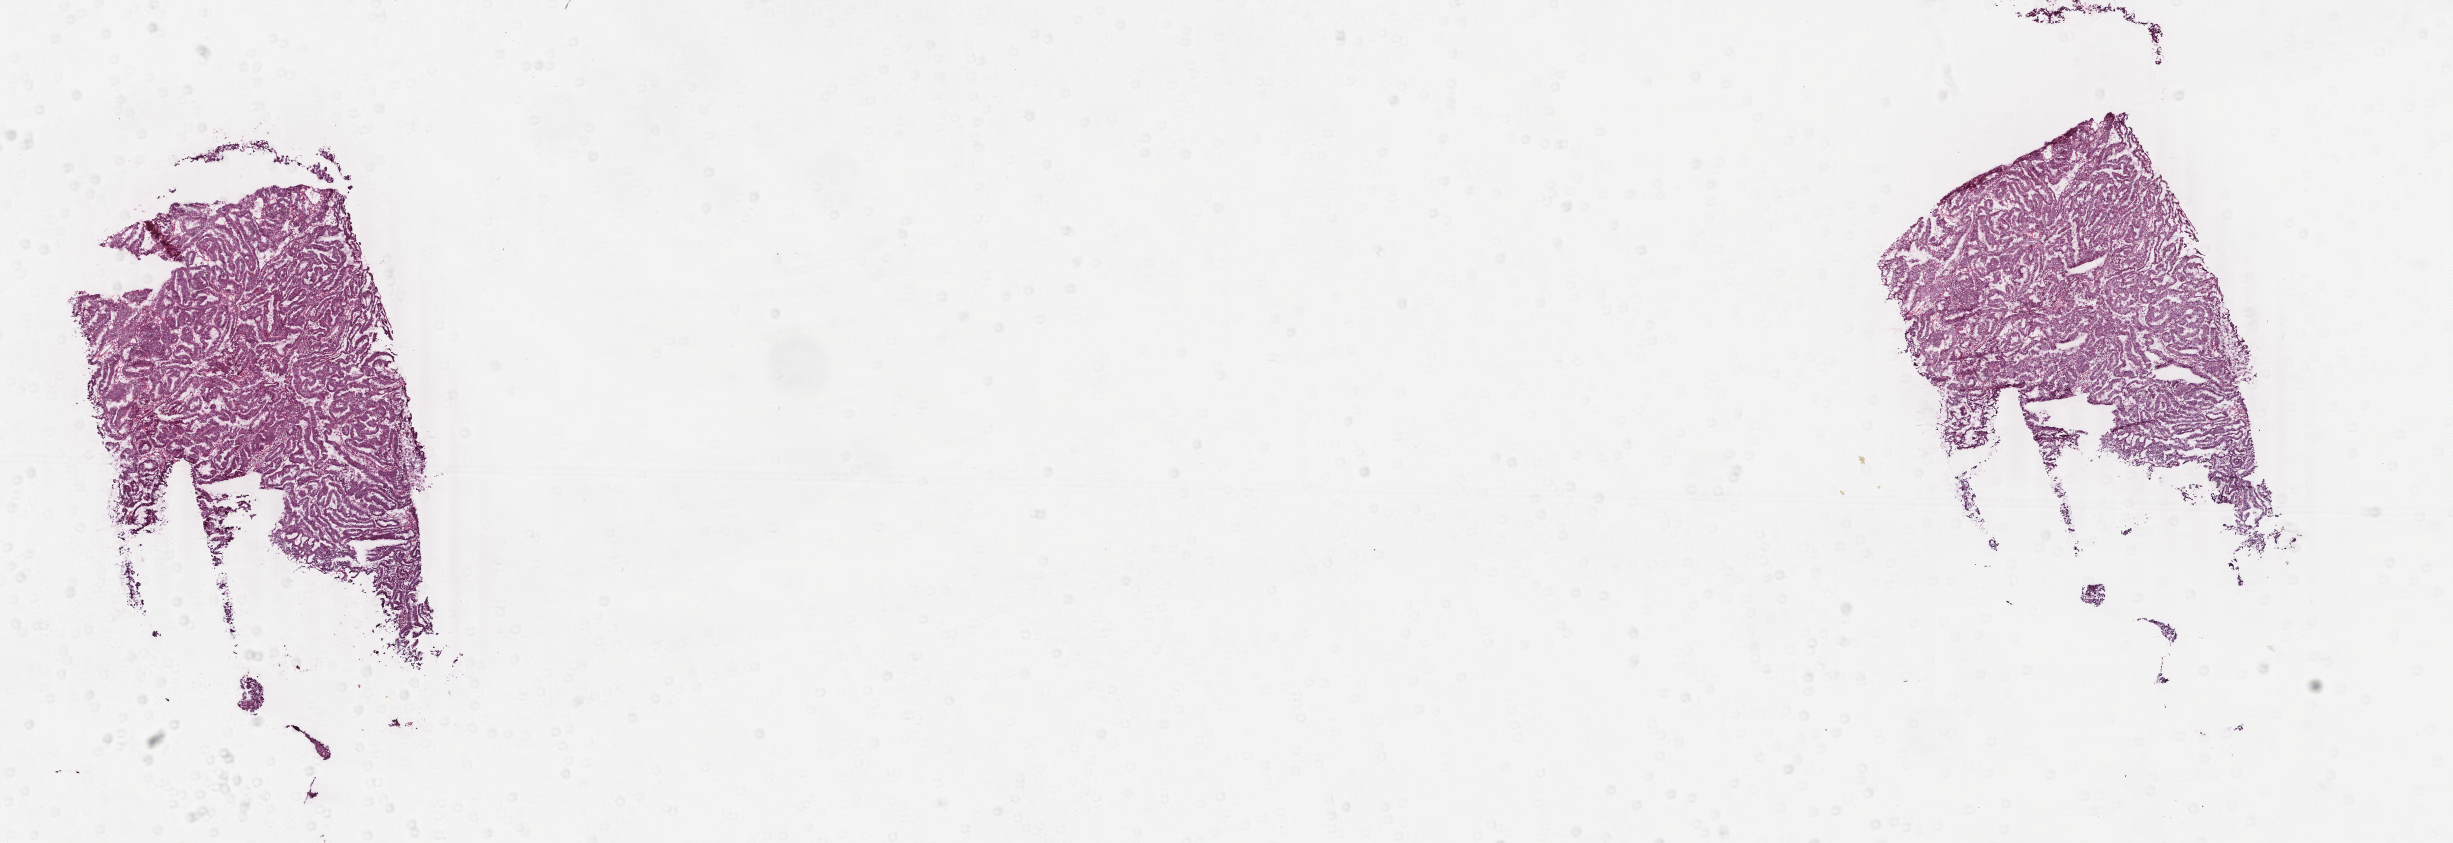
Whole-slide histology image, Hematoxylin and eosin (H&E) stained — shown as a low-resolution overview of the whole scanned area (about 19.5 x 6.7 mm, acquisition: 40x scan); frozen section from the bottom of the tissue portion; primary tumour sample from the uterus. Female patient; age at initial diagnosis 57 years. Histologic grade: G1 (well differentiated). Slide review estimates, as recorded: tumour cells 96%, tumour nuclei 96%, normal cells 0%, stromal cells 2%, necrosis 2%. Inflammatory infiltration, as recorded: lymphocyte infiltration 0%, monocyte infiltration 0%, neutrophil infiltration 2%.
* FIGO stage: IB
* pathologic diagnosis: Endometrioid adenocarcinoma, NOS (endometrium)